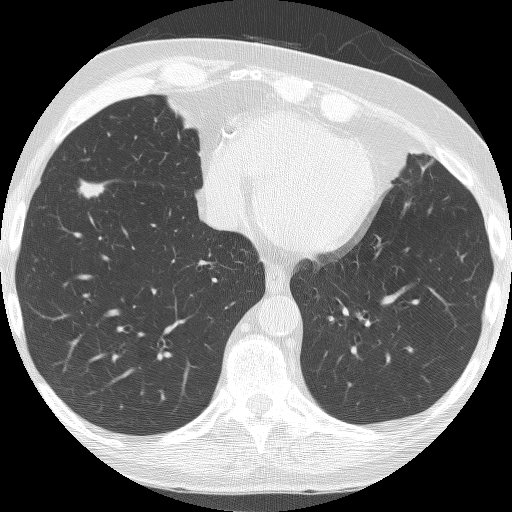
Axial slice from a low-dose chest CT screening exam. First (baseline) screen. Lung window (W 1500 / L -600 HU). Lung (sharp) reconstruction kernel (BONE). Slice 114 of 182 in the series. 512 × 512 image matrix. Male participant, aged 74 years at enrolment. Former smoker at enrolment.
Lesion marked by an expert reader, bounding box (x1, y1, x2, y2) in pixels: (72, 170, 119, 207). The screening reader recorded 4 non-calcified nodules or masses ≥4 mm on this exam; which of them this box marks is not recorded. Participant outcome: lung cancer diagnosed 35 days after this screen — bronchiolo-alveolar carcinoma, mucinous, right lower lobe, well differentiated (G1), stage IA (AJCC 6th edition), 22 mm at pathology.